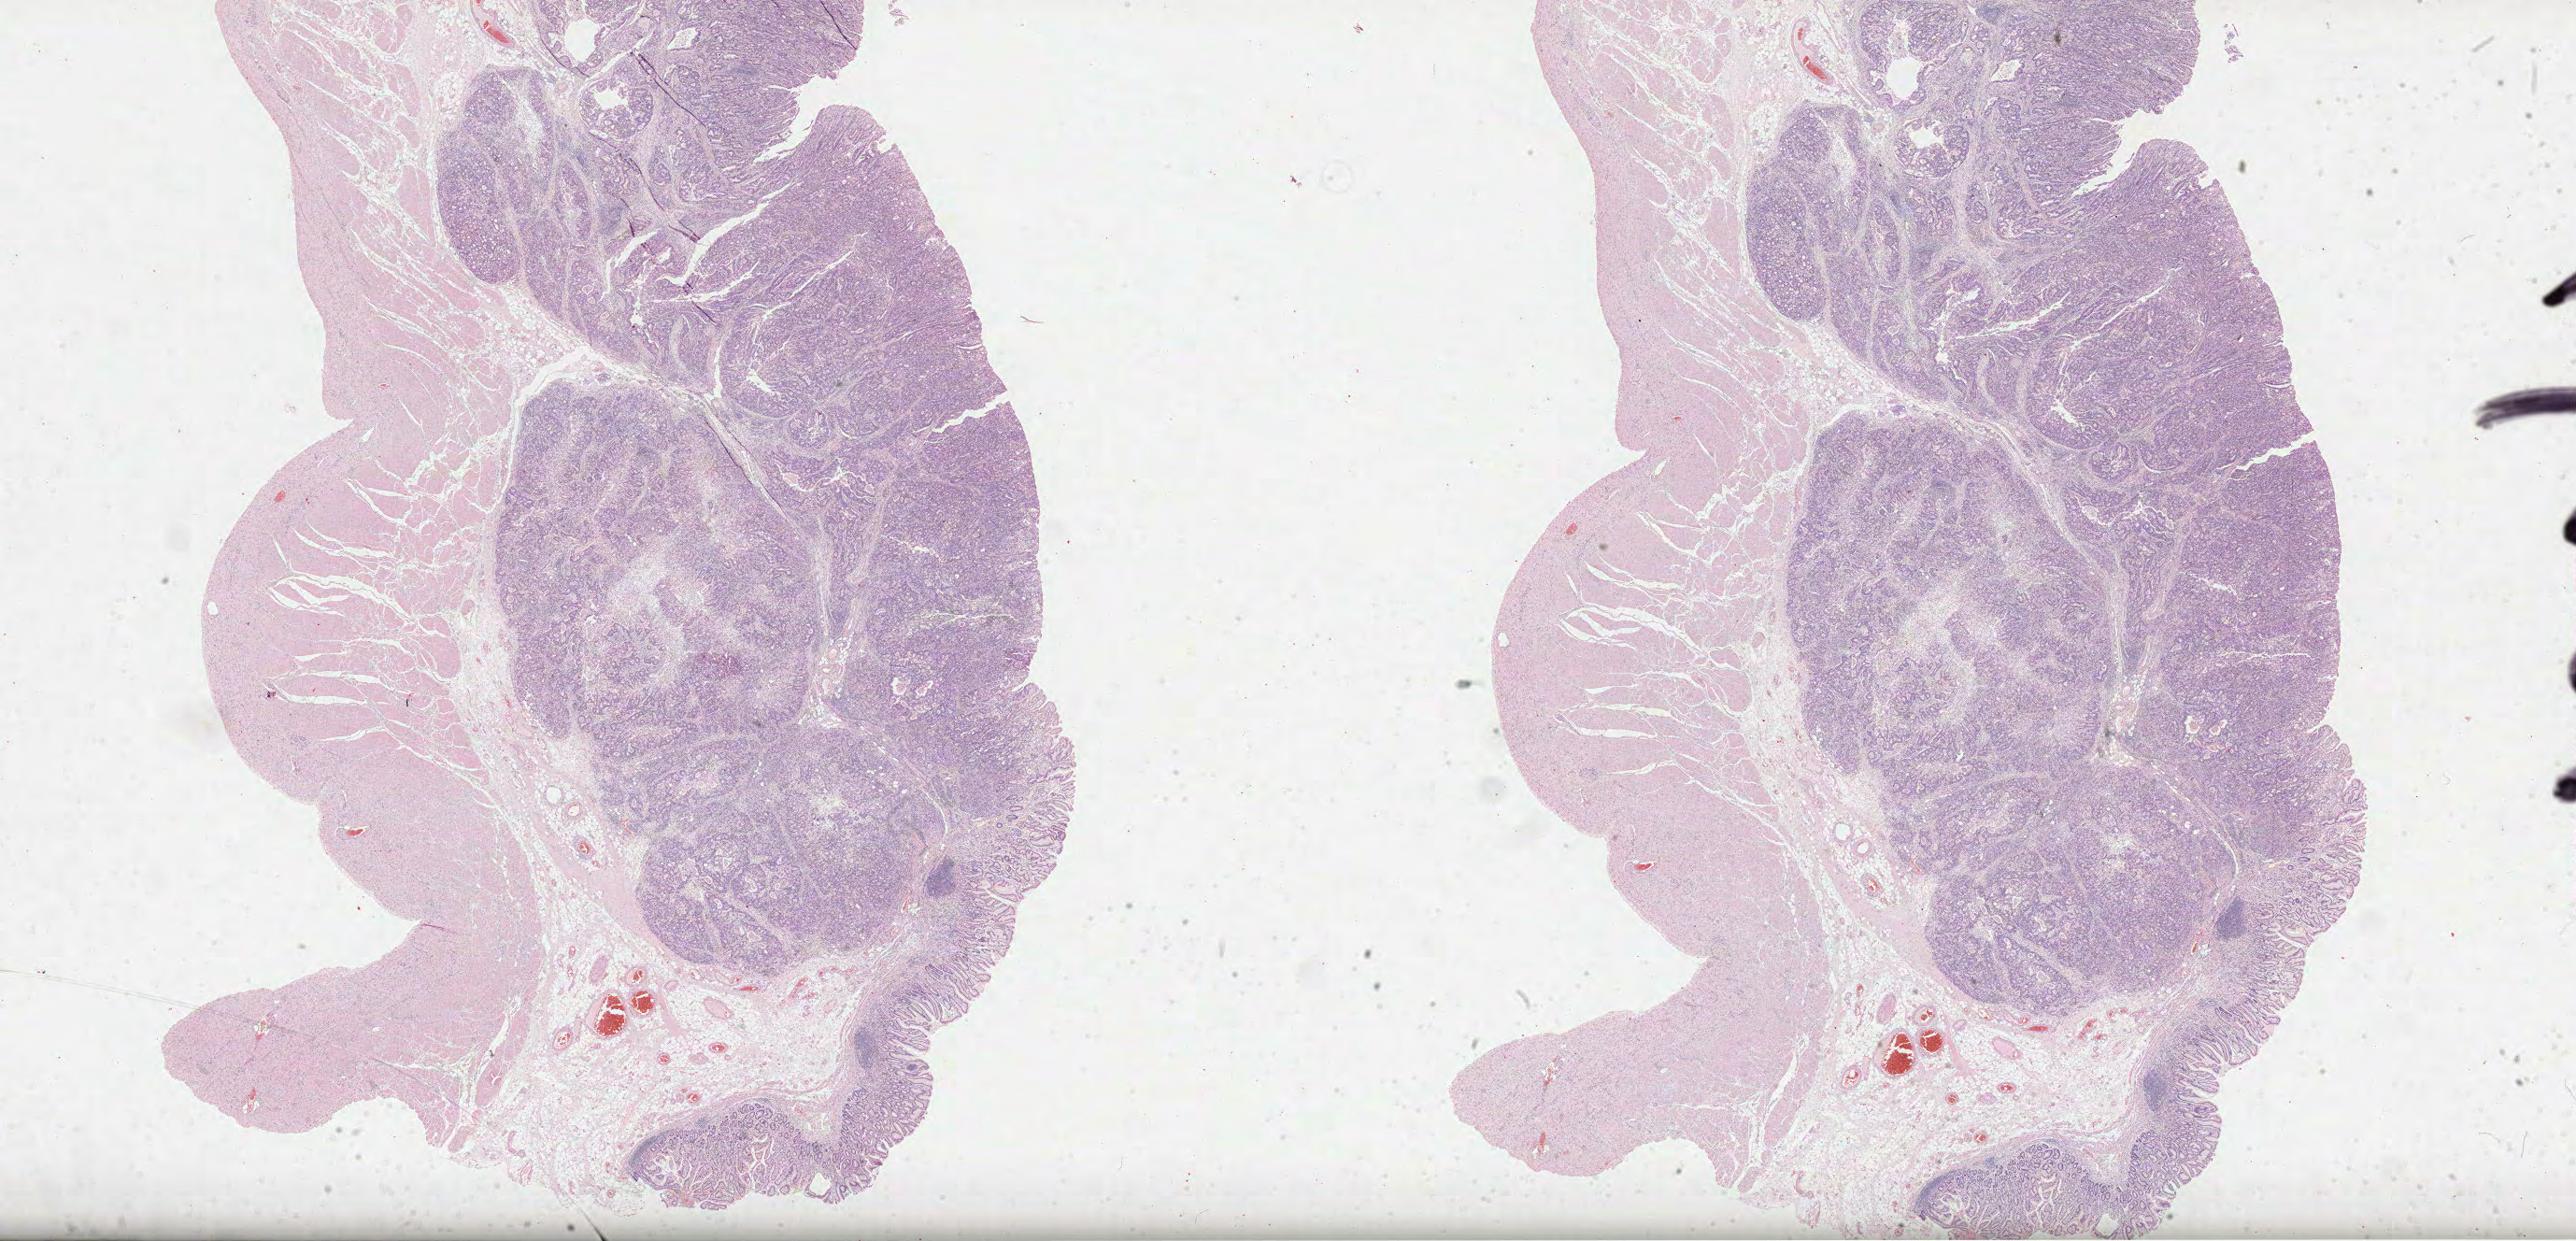
Digitized H&E-stained tissue section (whole slide), shown as a low-resolution overview of the whole scanned area (about 44.5 x 21.4 mm); FFPE section; stomach, primary tumour sample. Male patient; age at initial diagnosis 80 years. Histologic grade: G3 (poorly differentiated).
- lymph nodes positive (case pathology): 6 of 19 examined
- AJCC pathologic stage: IIIA (7th edition)
- pathologic diagnosis: Tubular adenocarcinoma